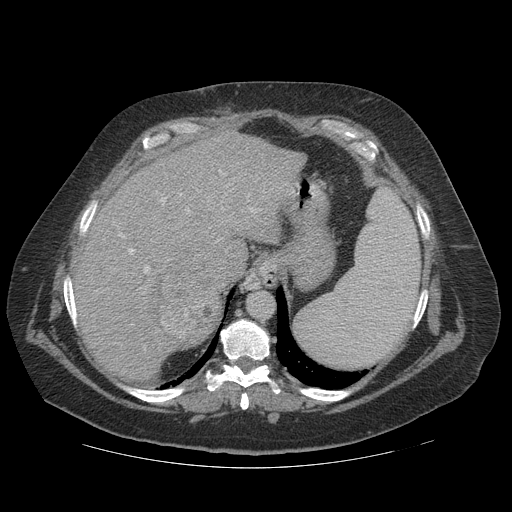
Contrast-enhanced abdominal CT (liver protocol), one axial slice; position 89 of 121 along the scan axis; reconstruction kernel STANDARD; 140 kVp; soft-tissue window (W 400 / L 40 HU); 2.5 mm slice thickness; 512 × 512 image matrix, field of view 420 × 420 mm. Case-level facts recorded for this patient, not image findings: diagnosis: hepatocellular carcinoma (patient treated with transarterial chemoembolisation; whether this scan precedes or follows treatment is not stated here); TNM stage (as recorded): Stage-IIIA; Child-Pugh class: A; tumour differentiation: well differentiated; tumour size: 7.4 cm.
Structures marked on this image (semi-automatically segmented with operator editing):
- liver parenchyma outside the tumour (the mass and vessels are separate outlines, so this box may not span the whole liver): bounding box [x1, y1, x2, y2] px = [74, 130, 305, 380]
- mass: [144, 264, 221, 351]
- liver vessels: [96, 169, 295, 349]